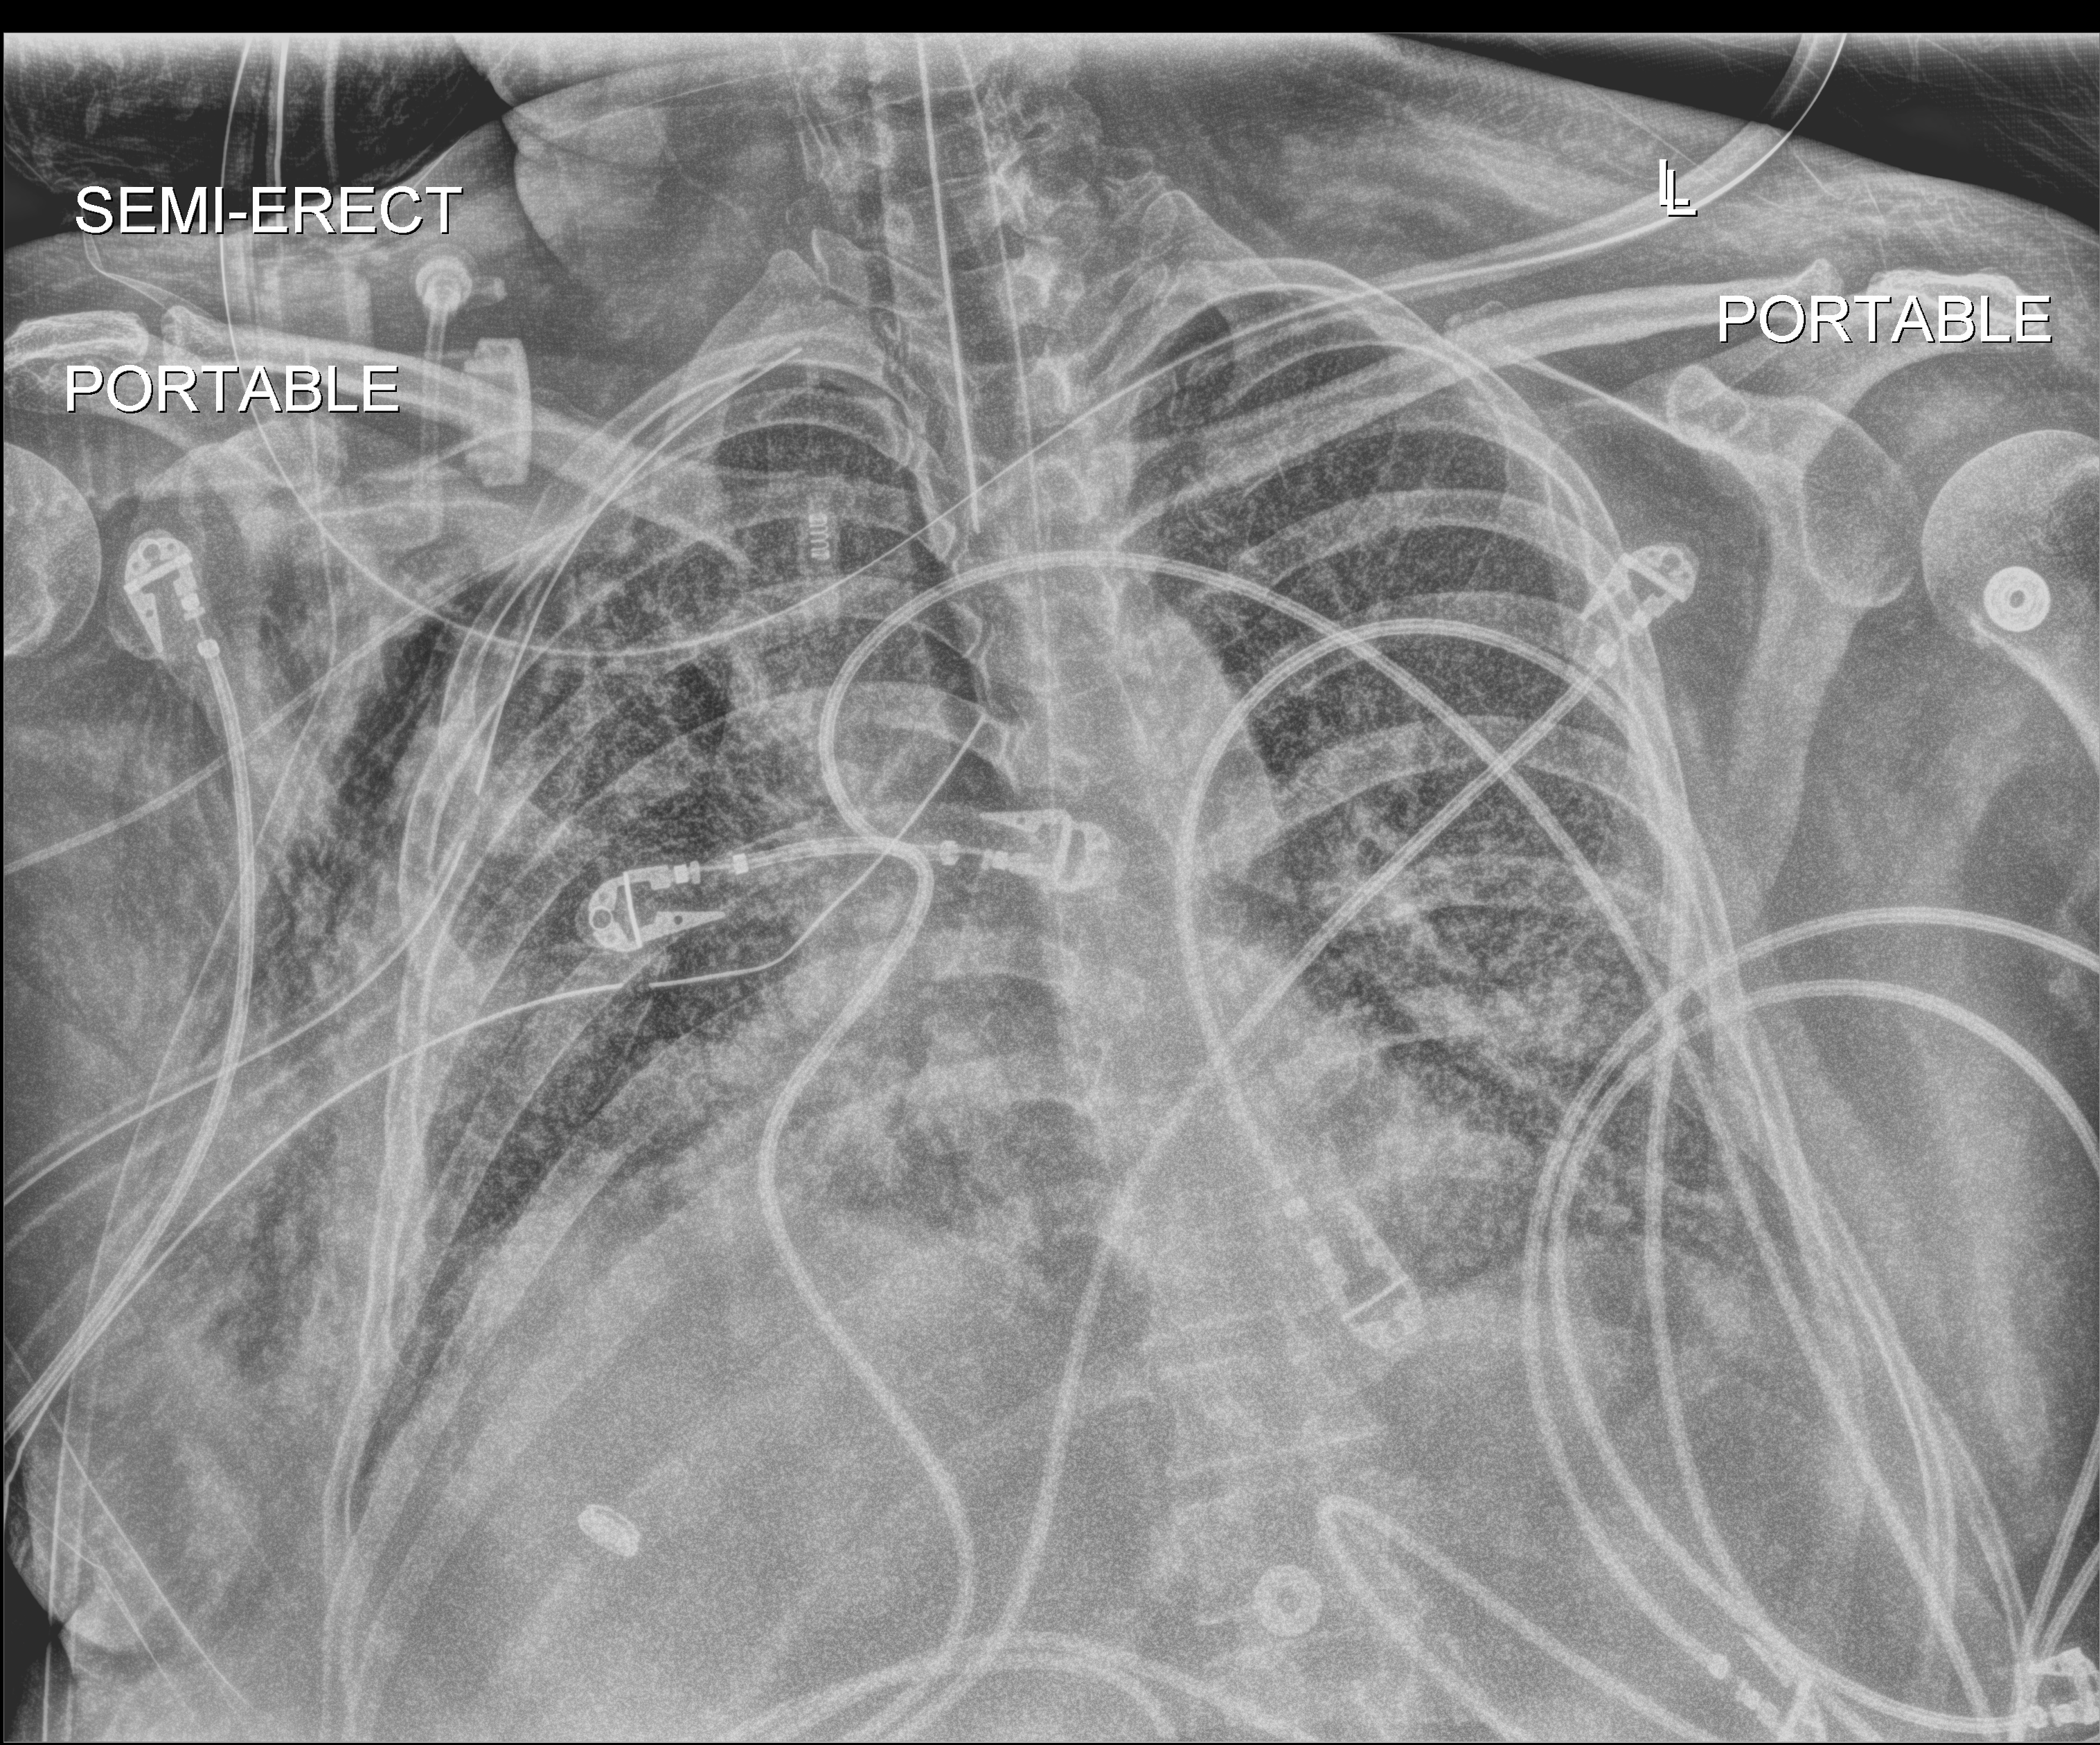
Bedside chest radiograph (digital radiography), anteroposterior (AP) projection. Adult patient hospitalised with COVID-19, age 18–59 years.
Admission-level facts for this patient (not findings on this image; timing relative to this image not recorded): admitted to intensive care during this hospital stay: yes; smoking status (admission record): never.